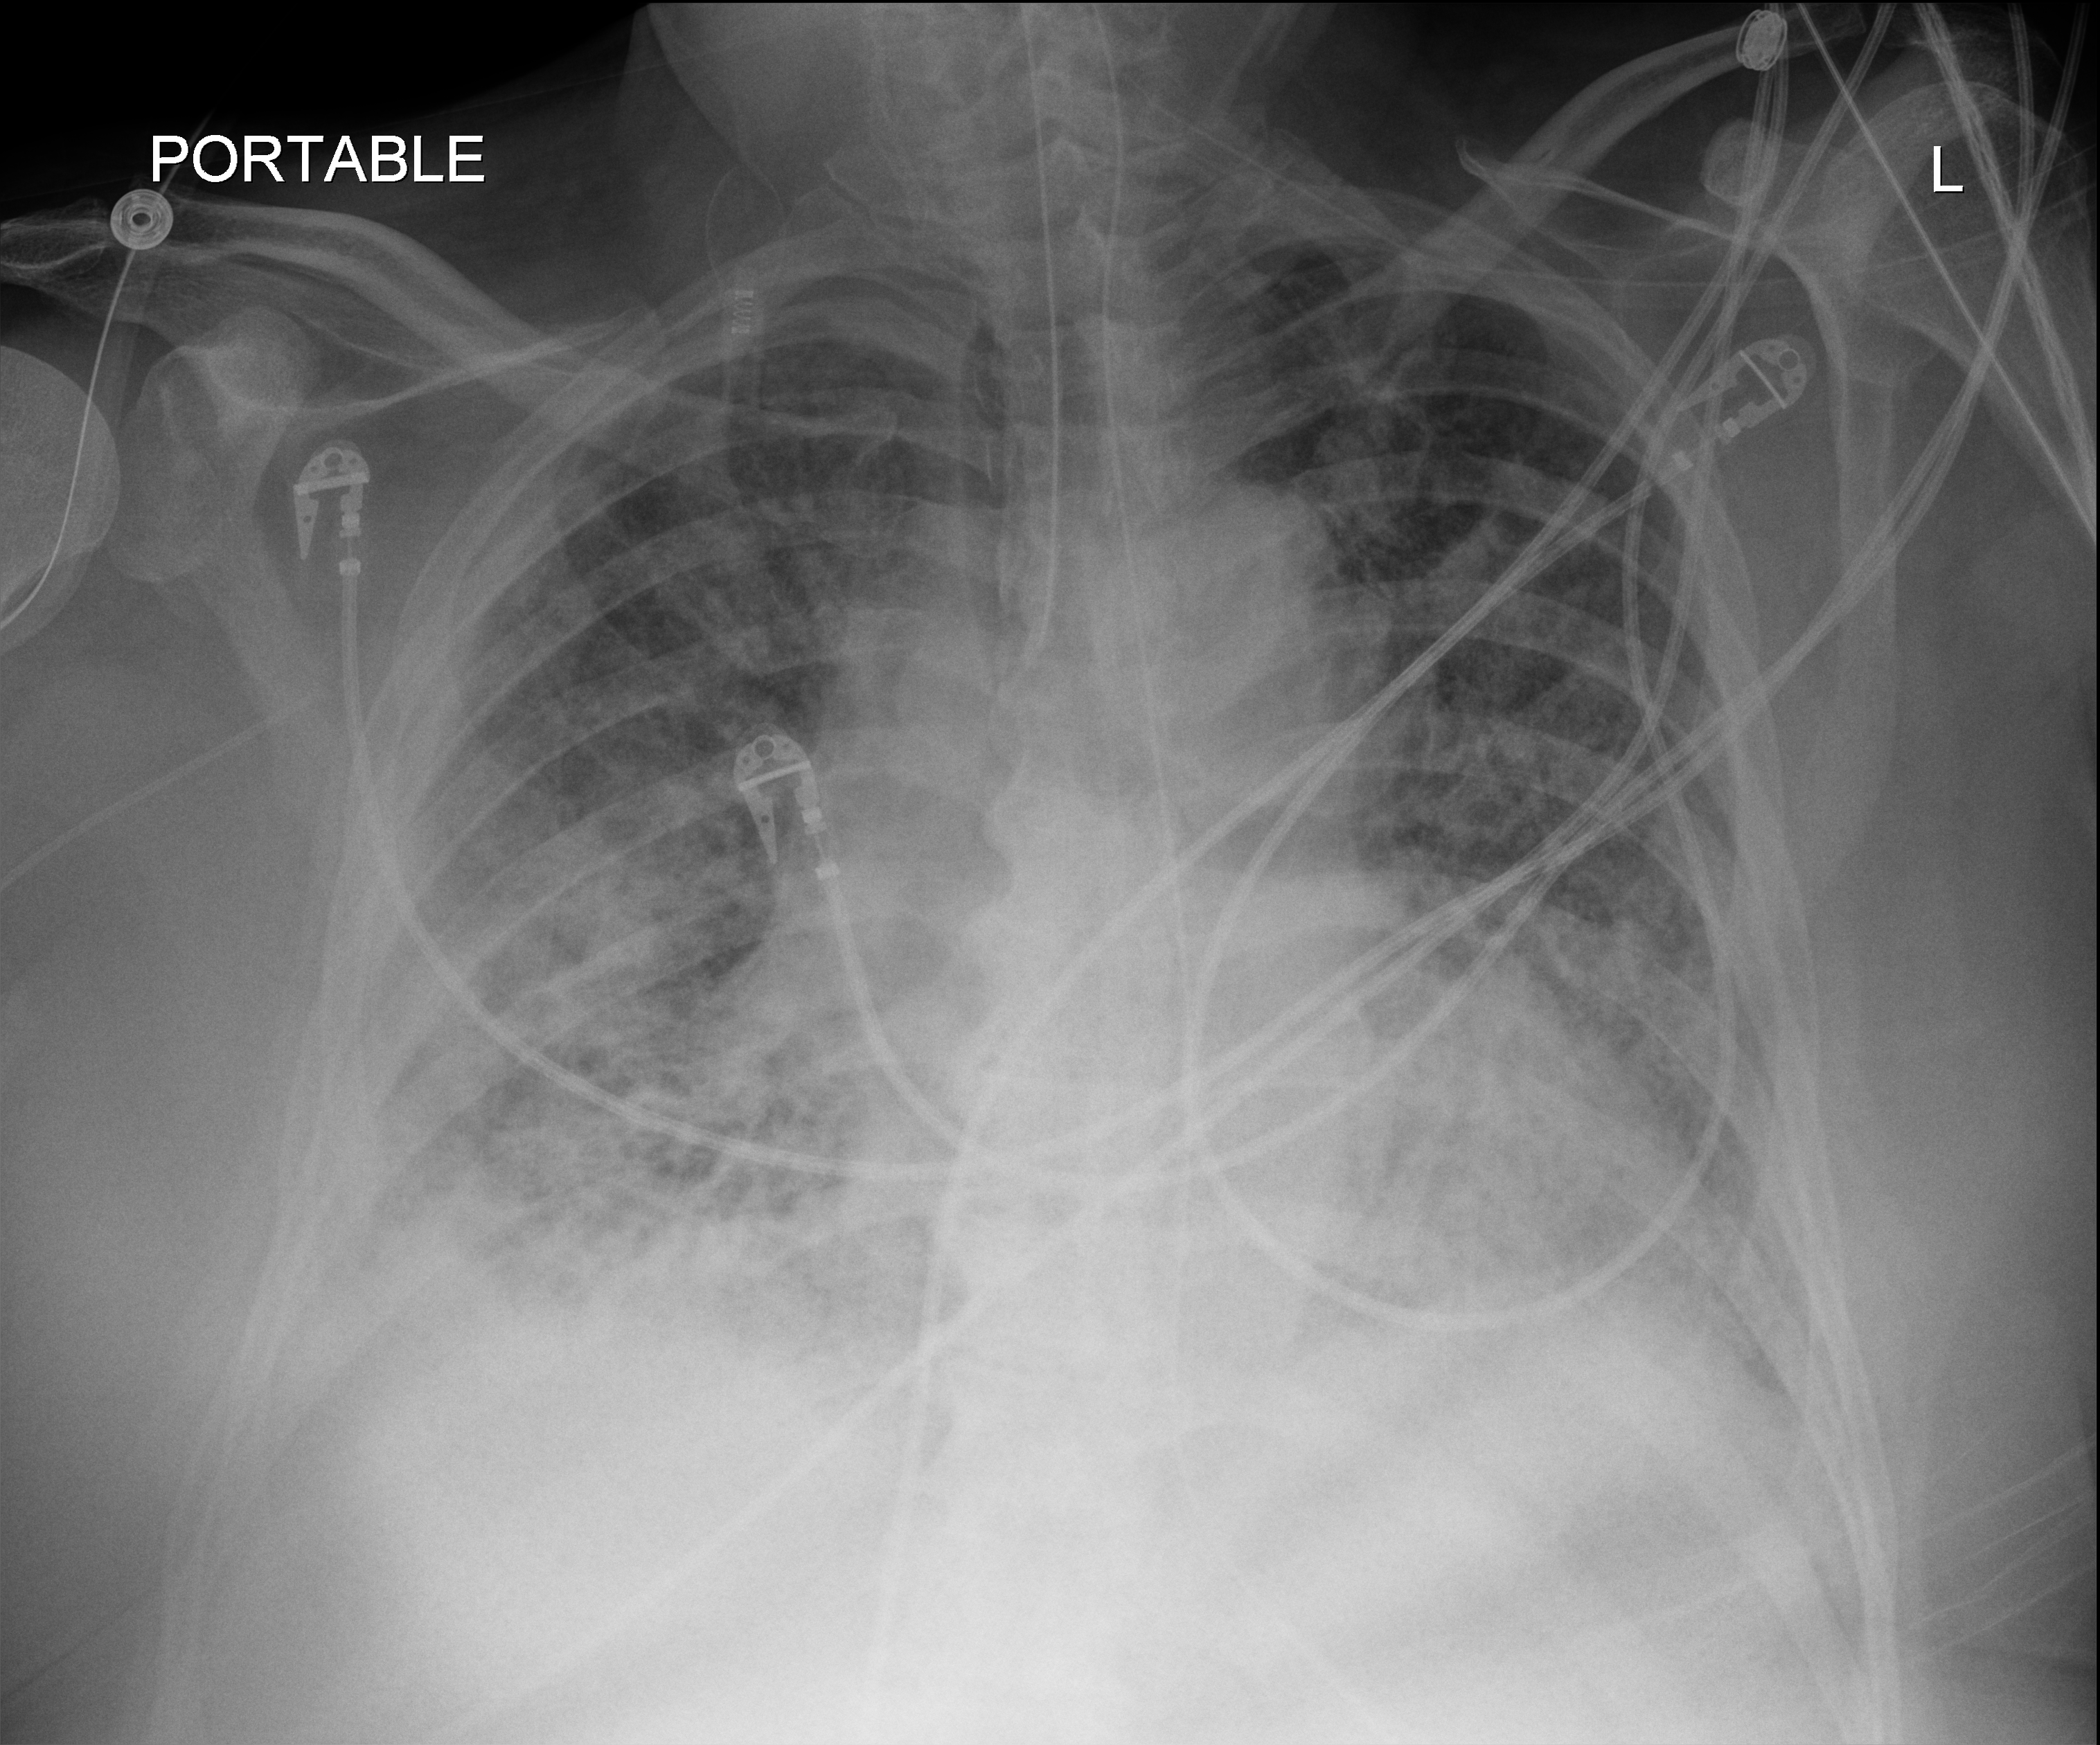
Bedside chest radiograph (digital radiography); anteroposterior (AP) projection. Male patient hospitalised with COVID-19, age 60–74 years.
Hospital-stay facts (about this admission, not read from this image; timing relative to this image not recorded): hypertension (admission record): yes; admitted to intensive care during this hospital stay: yes; chronic kidney disease (admission record): no.